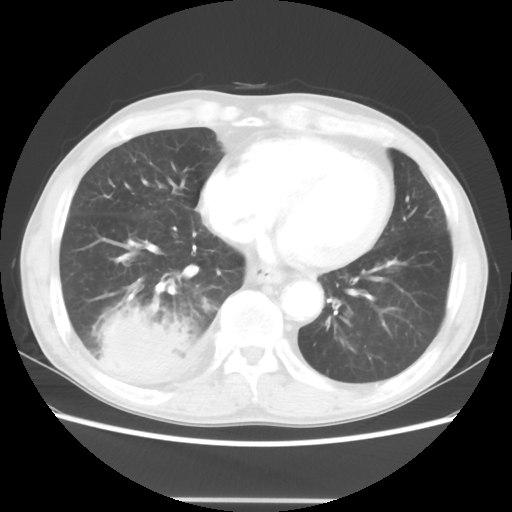
Chest CT, one axial slice; position 13 of 48 along the scan axis; reconstruction kernel STANDARD; 100 kVp; lung window (W 1500 / L -600 HU); 5 mm slice thickness; 512 × 512 image matrix, field of view 361 × 361 mm. Male patient, age 66 years. From the clinical record (not read from this slice): clinical TNM (as recorded): T4 N1 M1; histopathological grade: G3.
Outlined on this slice (bounding box drawn by a radiologist):
- lung tumour (recorded histology: small cell carcinoma): box from (x=94, y=298) to (x=195, y=401) px